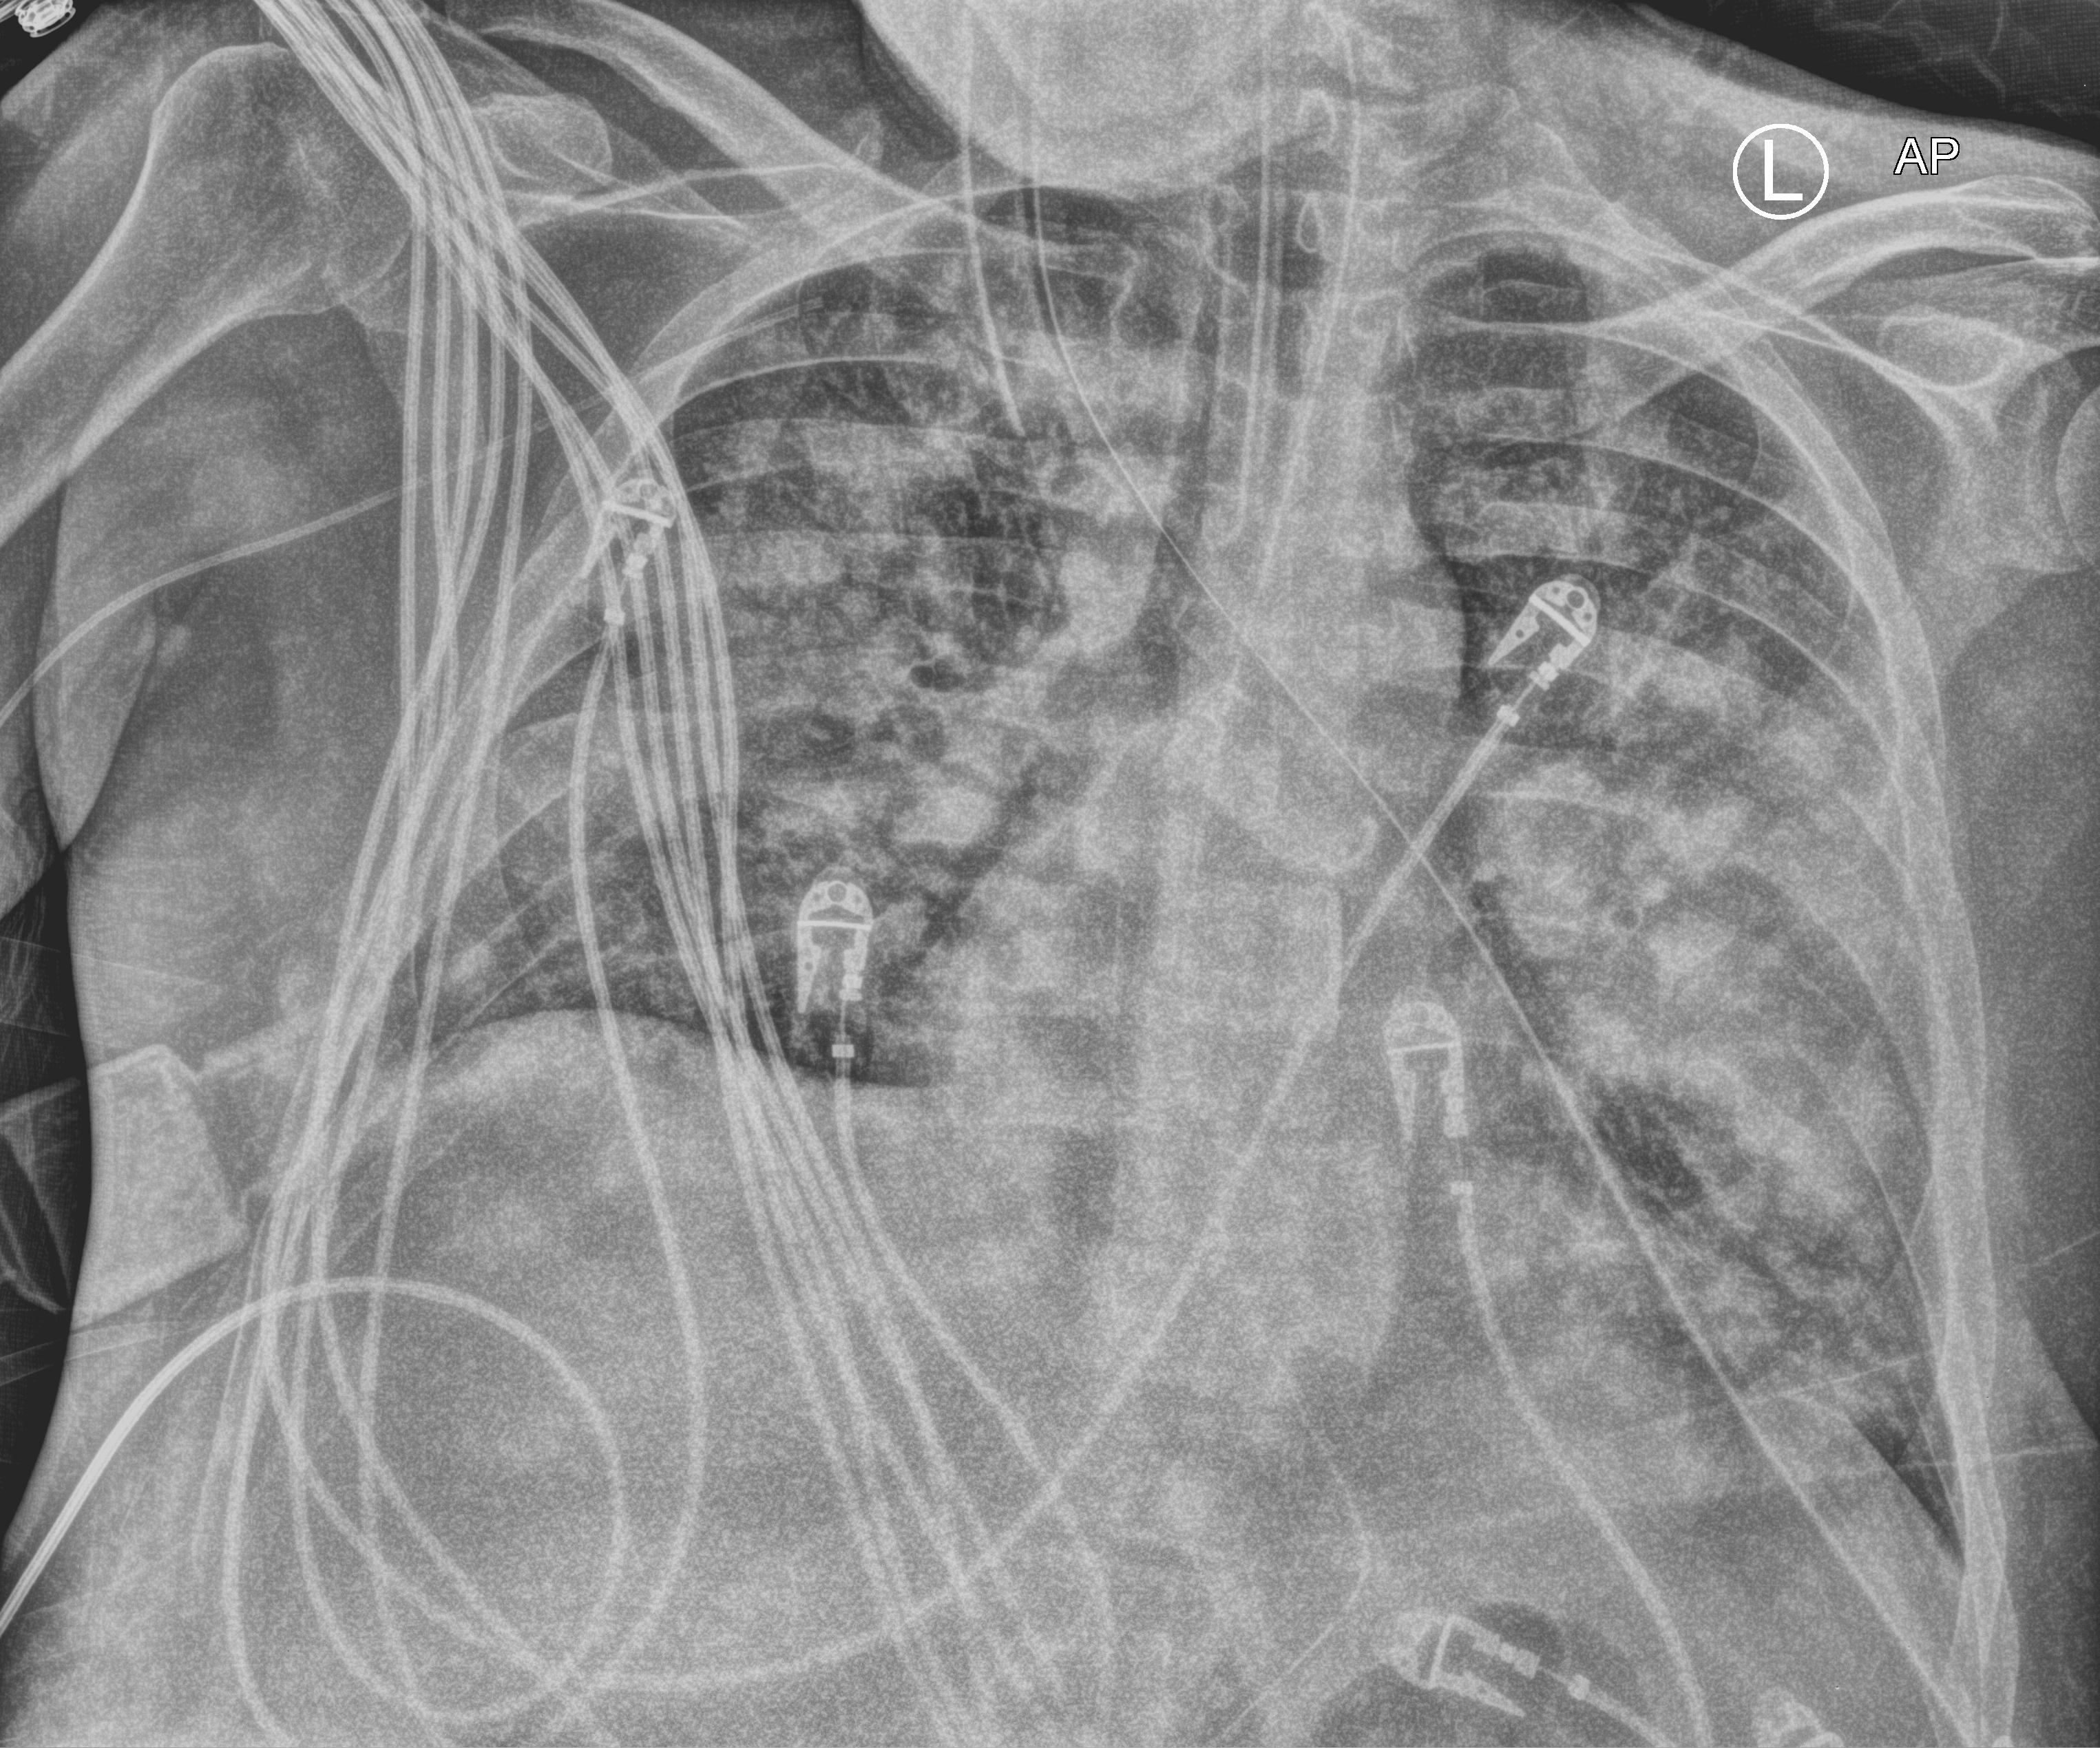
Bedside chest radiograph (computed radiography); anteroposterior (AP) projection. Male patient hospitalised with COVID-19, age 18–59 years.
Admission-level facts for this patient (not findings on this image; timing relative to this image not recorded): admitted to intensive care during this hospital stay: yes.